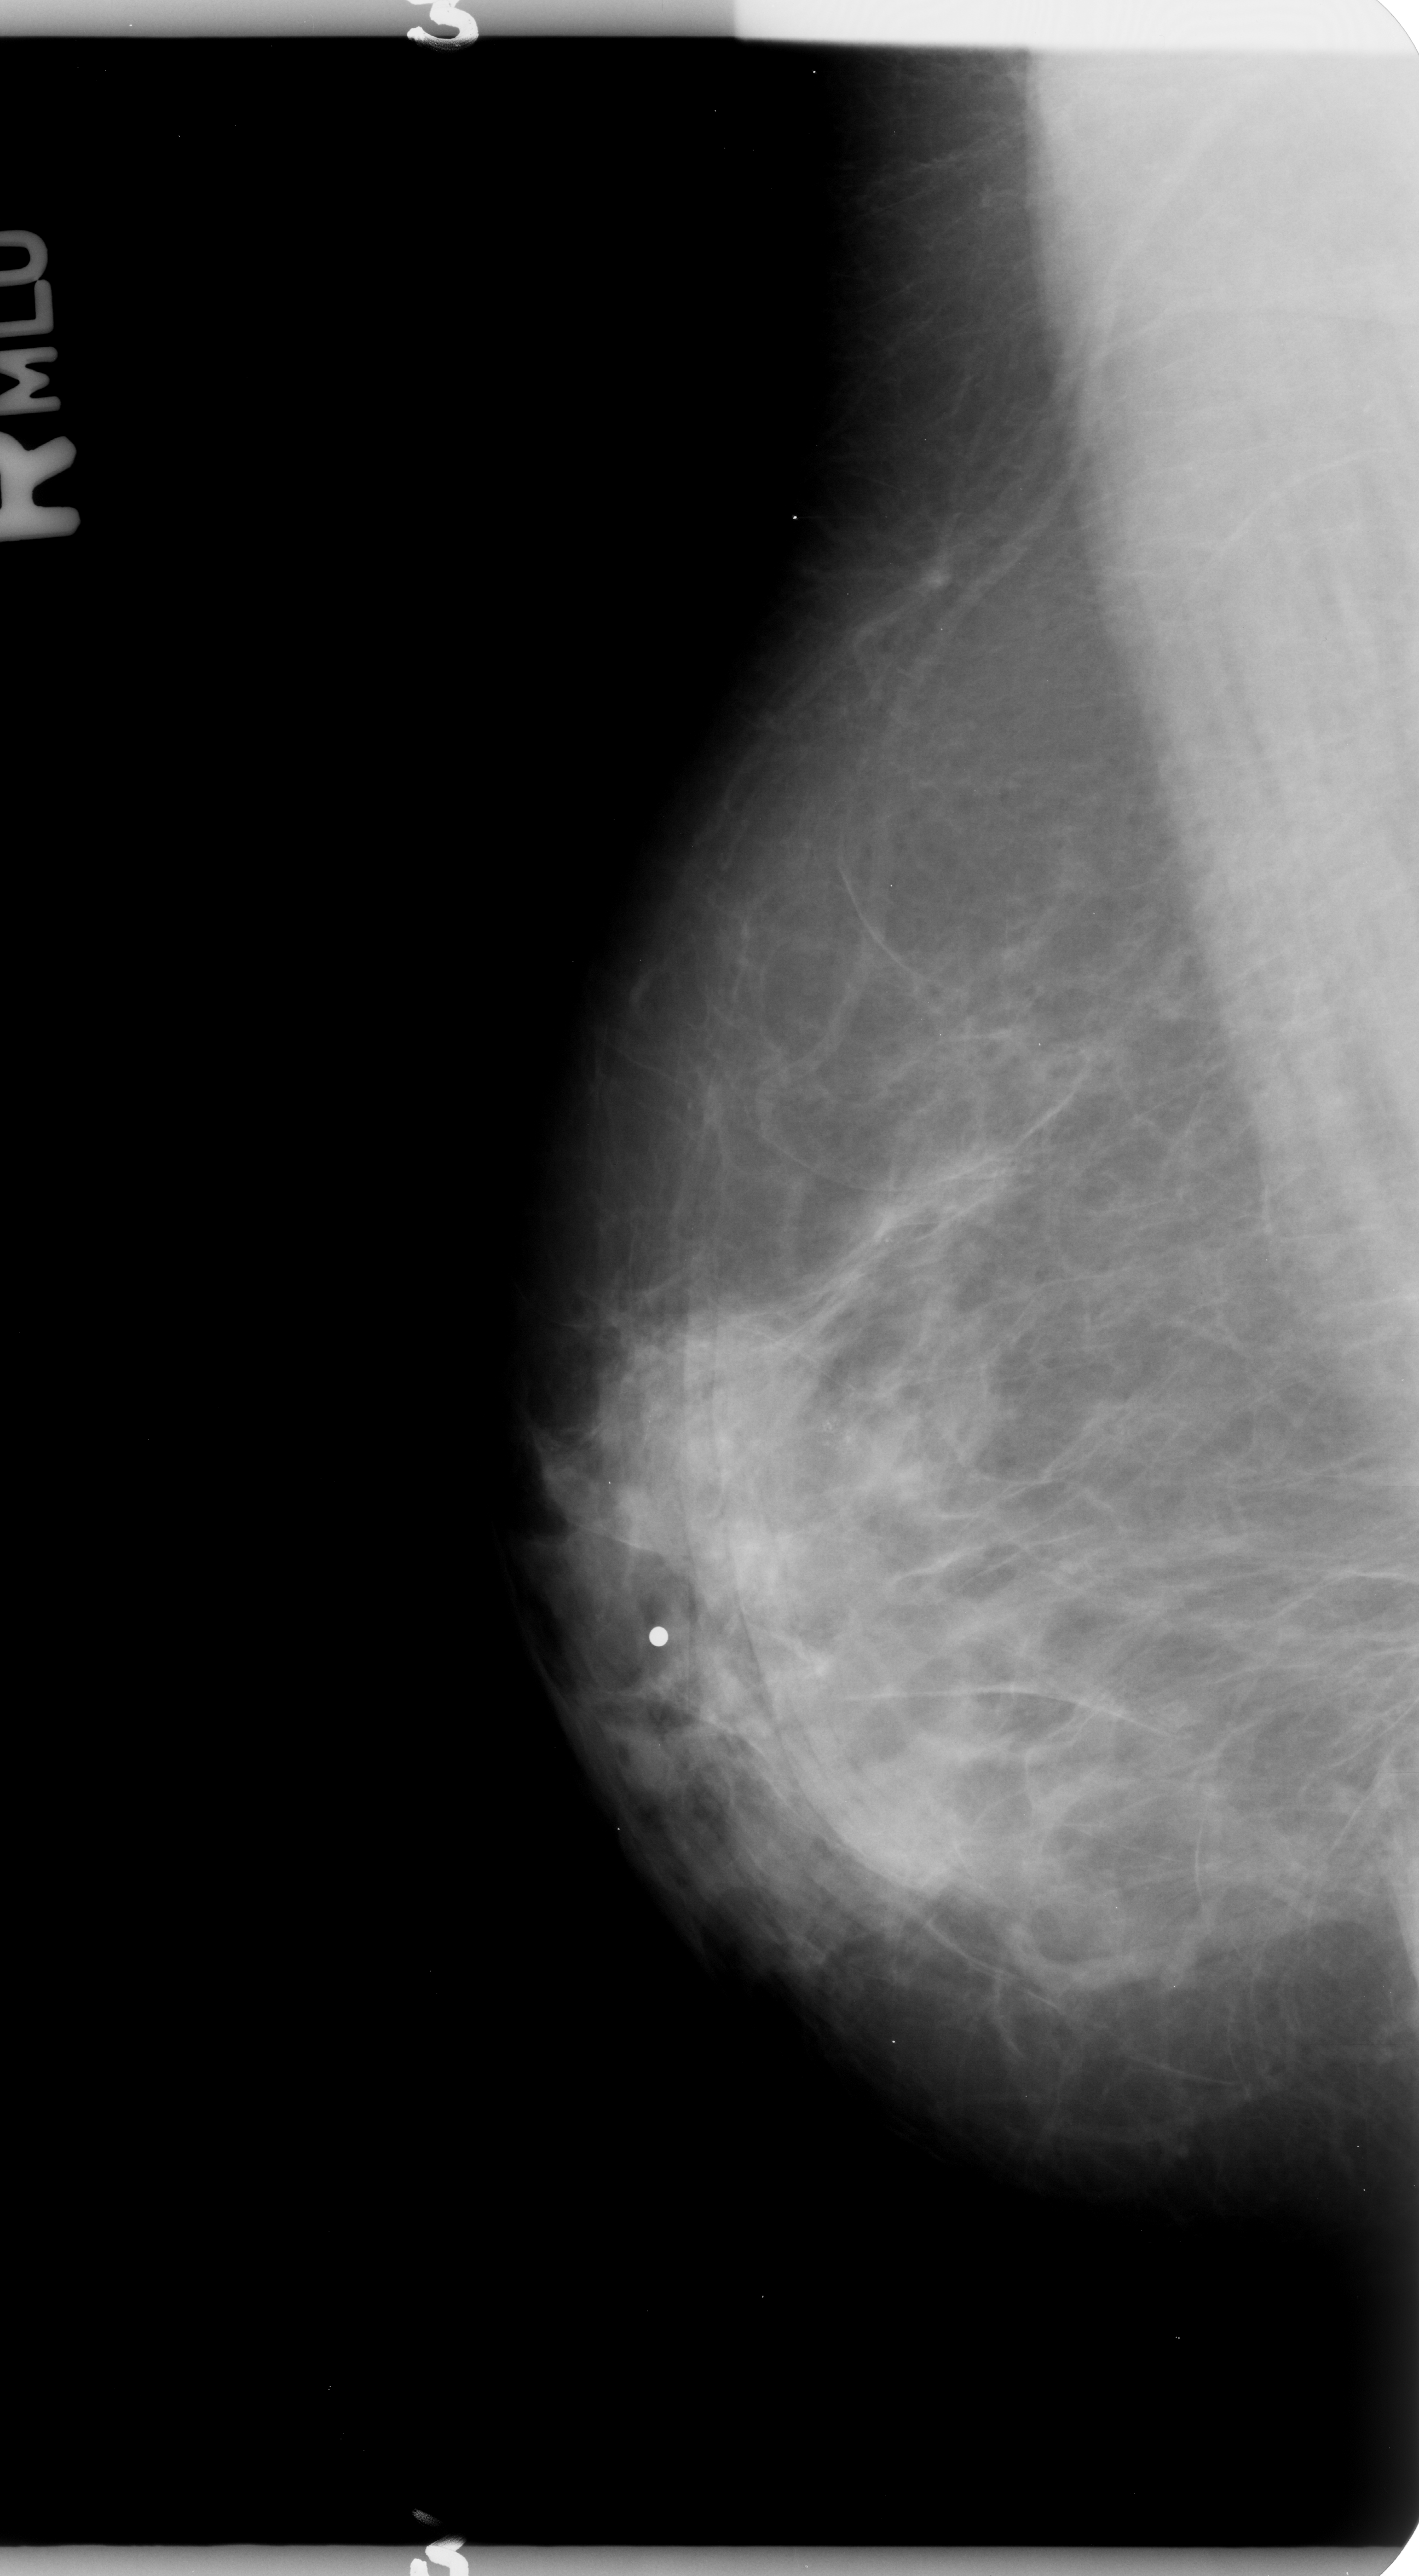
Mammogram (digitized film), right breast, mediolateral oblique (MLO) view, BI-RADS breast density category 3 (scale 1–4).
Marked abnormality: calcifications, morphology pleomorphic, distribution clustered; BI-RADS assessment category 4; subtlety rating 3 on a 1 (subtle) to 5 (obvious) scale; pathology result (as recorded, not read from the image): benign.